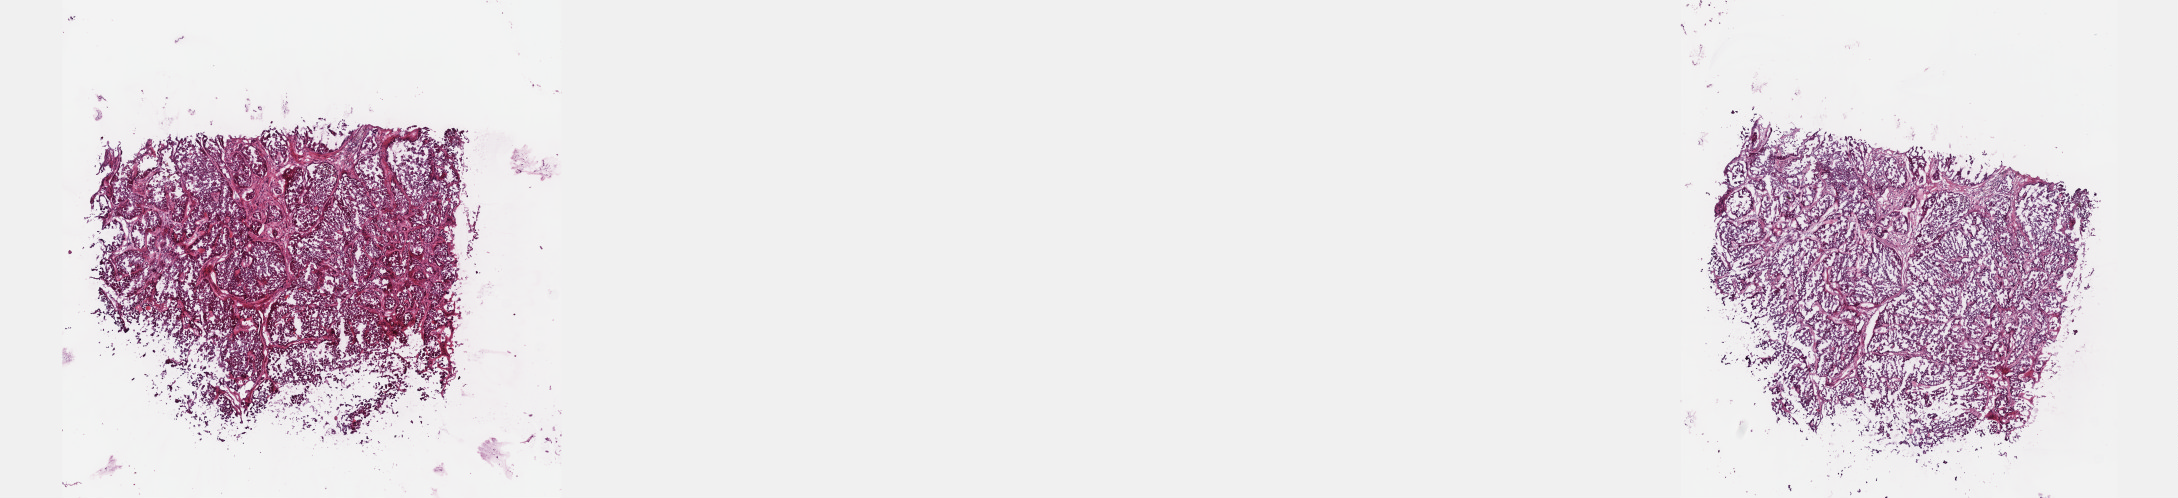
Hematoxylin and eosin (H&E) stained whole-slide image — shown as a low-resolution overview of the whole scanned area (about 17.6 x 4.0 mm, slide scanned at 40x); frozen section from the top of the tissue portion; sample: primary tumour, kidney. Patient: male, age at initial diagnosis 60 years. Pathologist review of this section (percent, as recorded): tumour cells 100%, tumour nuclei 75%, normal cells 0%, stromal cells 0%, necrosis 0%. Inflammatory infiltration, as recorded: lymphocyte infiltration 1%, monocyte infiltration 1%, neutrophil infiltration 0%.
Histologic diagnosis: Papillary adenocarcinoma, NOS. Lymph nodes positive (case pathology): 1 of 2 examined. Laterality: left. AJCC pathologic stage: IV.